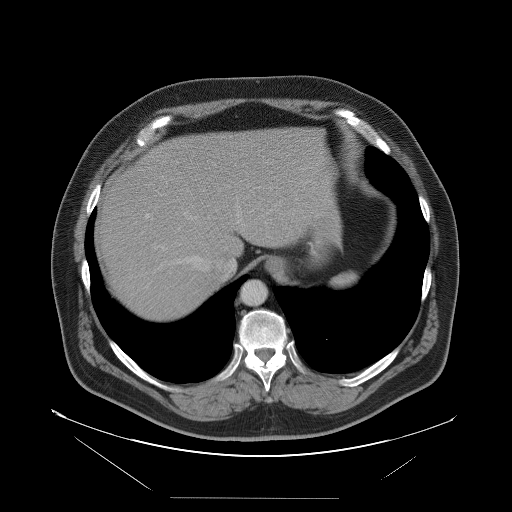
Contrast-enhanced abdominal CT, one axial slice. Position 82 of 114 along the scan axis. 120 kVp. Intravenous contrast given. Soft-tissue window (W 400 / L 40 HU). 5 mm slice thickness. 512 × 512 image matrix. Male patient, age 61 years. Case-level facts recorded for this patient, not image findings: diagnosis: colorectal cancer liver metastases, imaged before liver resection; multiple liver metastases: no; largest metastasis: 6.5 cm.
Annotated regions visible in this slice (manually delineated by an expert):
- hepatic veins: bounding box <168,209,273,277> (left, top, right, bottom; pixels)
- liver: <97,128,322,323>
- planned liver remnant (the part of the liver to remain after resection): <149,128,323,268>
- portal vein (with intrahepatic branches): <145,214,164,249>